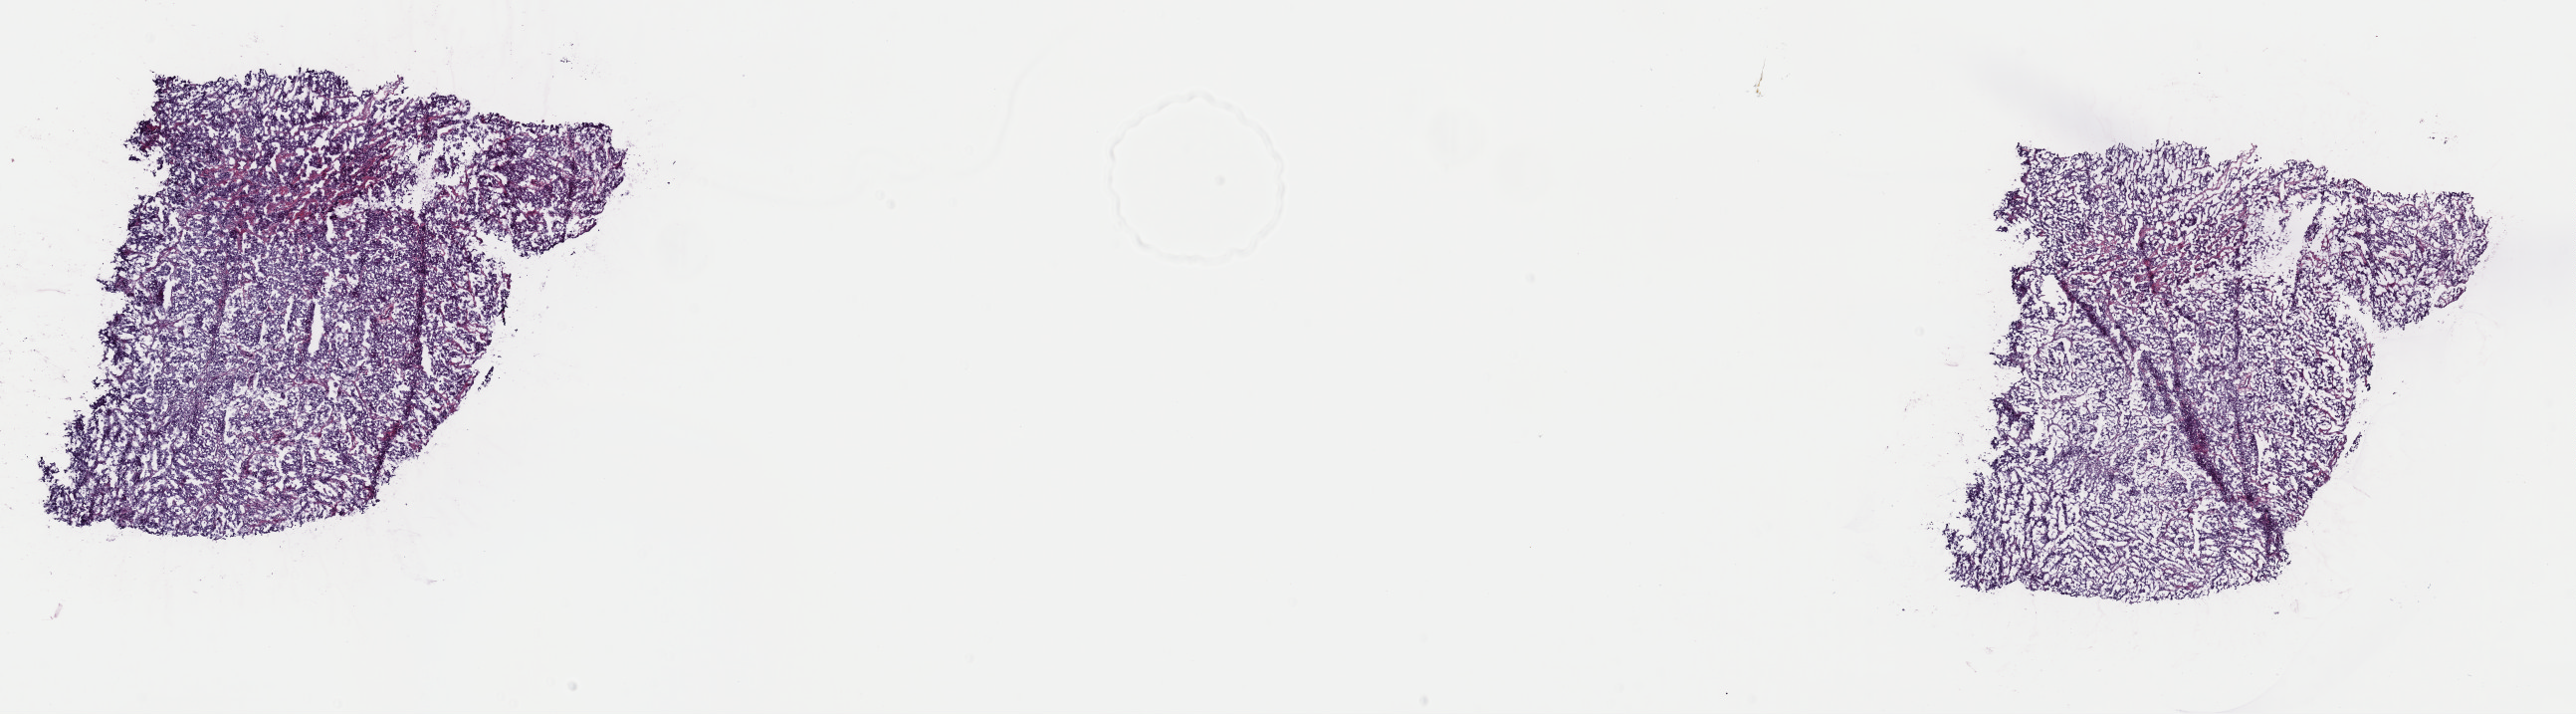
Whole-slide histology image, Hematoxylin and eosin (H&E) stained, whole scanned area (about 20.4 x 5.7 mm) shown as a low-resolution overview; frozen section from the top of the tissue portion; sample: primary tumour, bladder. Male patient; age at initial diagnosis 76 years. Histologic grade: high grade. Pathologist review of this section (percent, as recorded): tumour cells 75%, tumour nuclei 75%, normal cells 0%, stromal cells 21%, necrosis 4%. Inflammatory infiltration, as recorded: lymphocyte infiltration 3%, monocyte infiltration 2%, neutrophil infiltration 2%.
TNM: T4a N2 MX. Pathologic diagnosis: Transitional cell carcinoma. AJCC pathologic stage: IV (7th edition). Lymph nodes positive (case pathology): 2 of 47 examined.